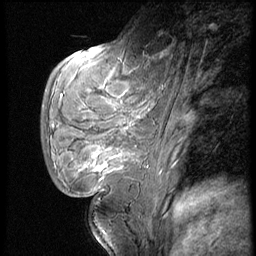
Breast MRI (dynamic contrast-enhanced), one sagittal slice. Slice 19 of 62 in the series (ordered by position). Dynamic contrast-enhanced series, image 2 of 4 at this slice position (ordered by acquisition). 1.5 T. TE 4.2 ms, TR 9 ms. 256 × 256 image matrix. Female patient, age 28 years. Case-level facts recorded for this patient, not image findings: setting: breast cancer imaged before/during neoadjuvant chemotherapy.
Outlined on this slice (semi-automatic segmentation, software-assisted and operator-edited):
- analysis volume of interest (the breast-tissue region the enhancement analysis was run in; not a lesion): bounding box [x1, y1, x2, y2] px = [47, 54, 150, 183]
- tumour enhancement mask (voxels above the 140 % enhancement threshold inside the analysis volume of interest): [80, 151, 124, 172]